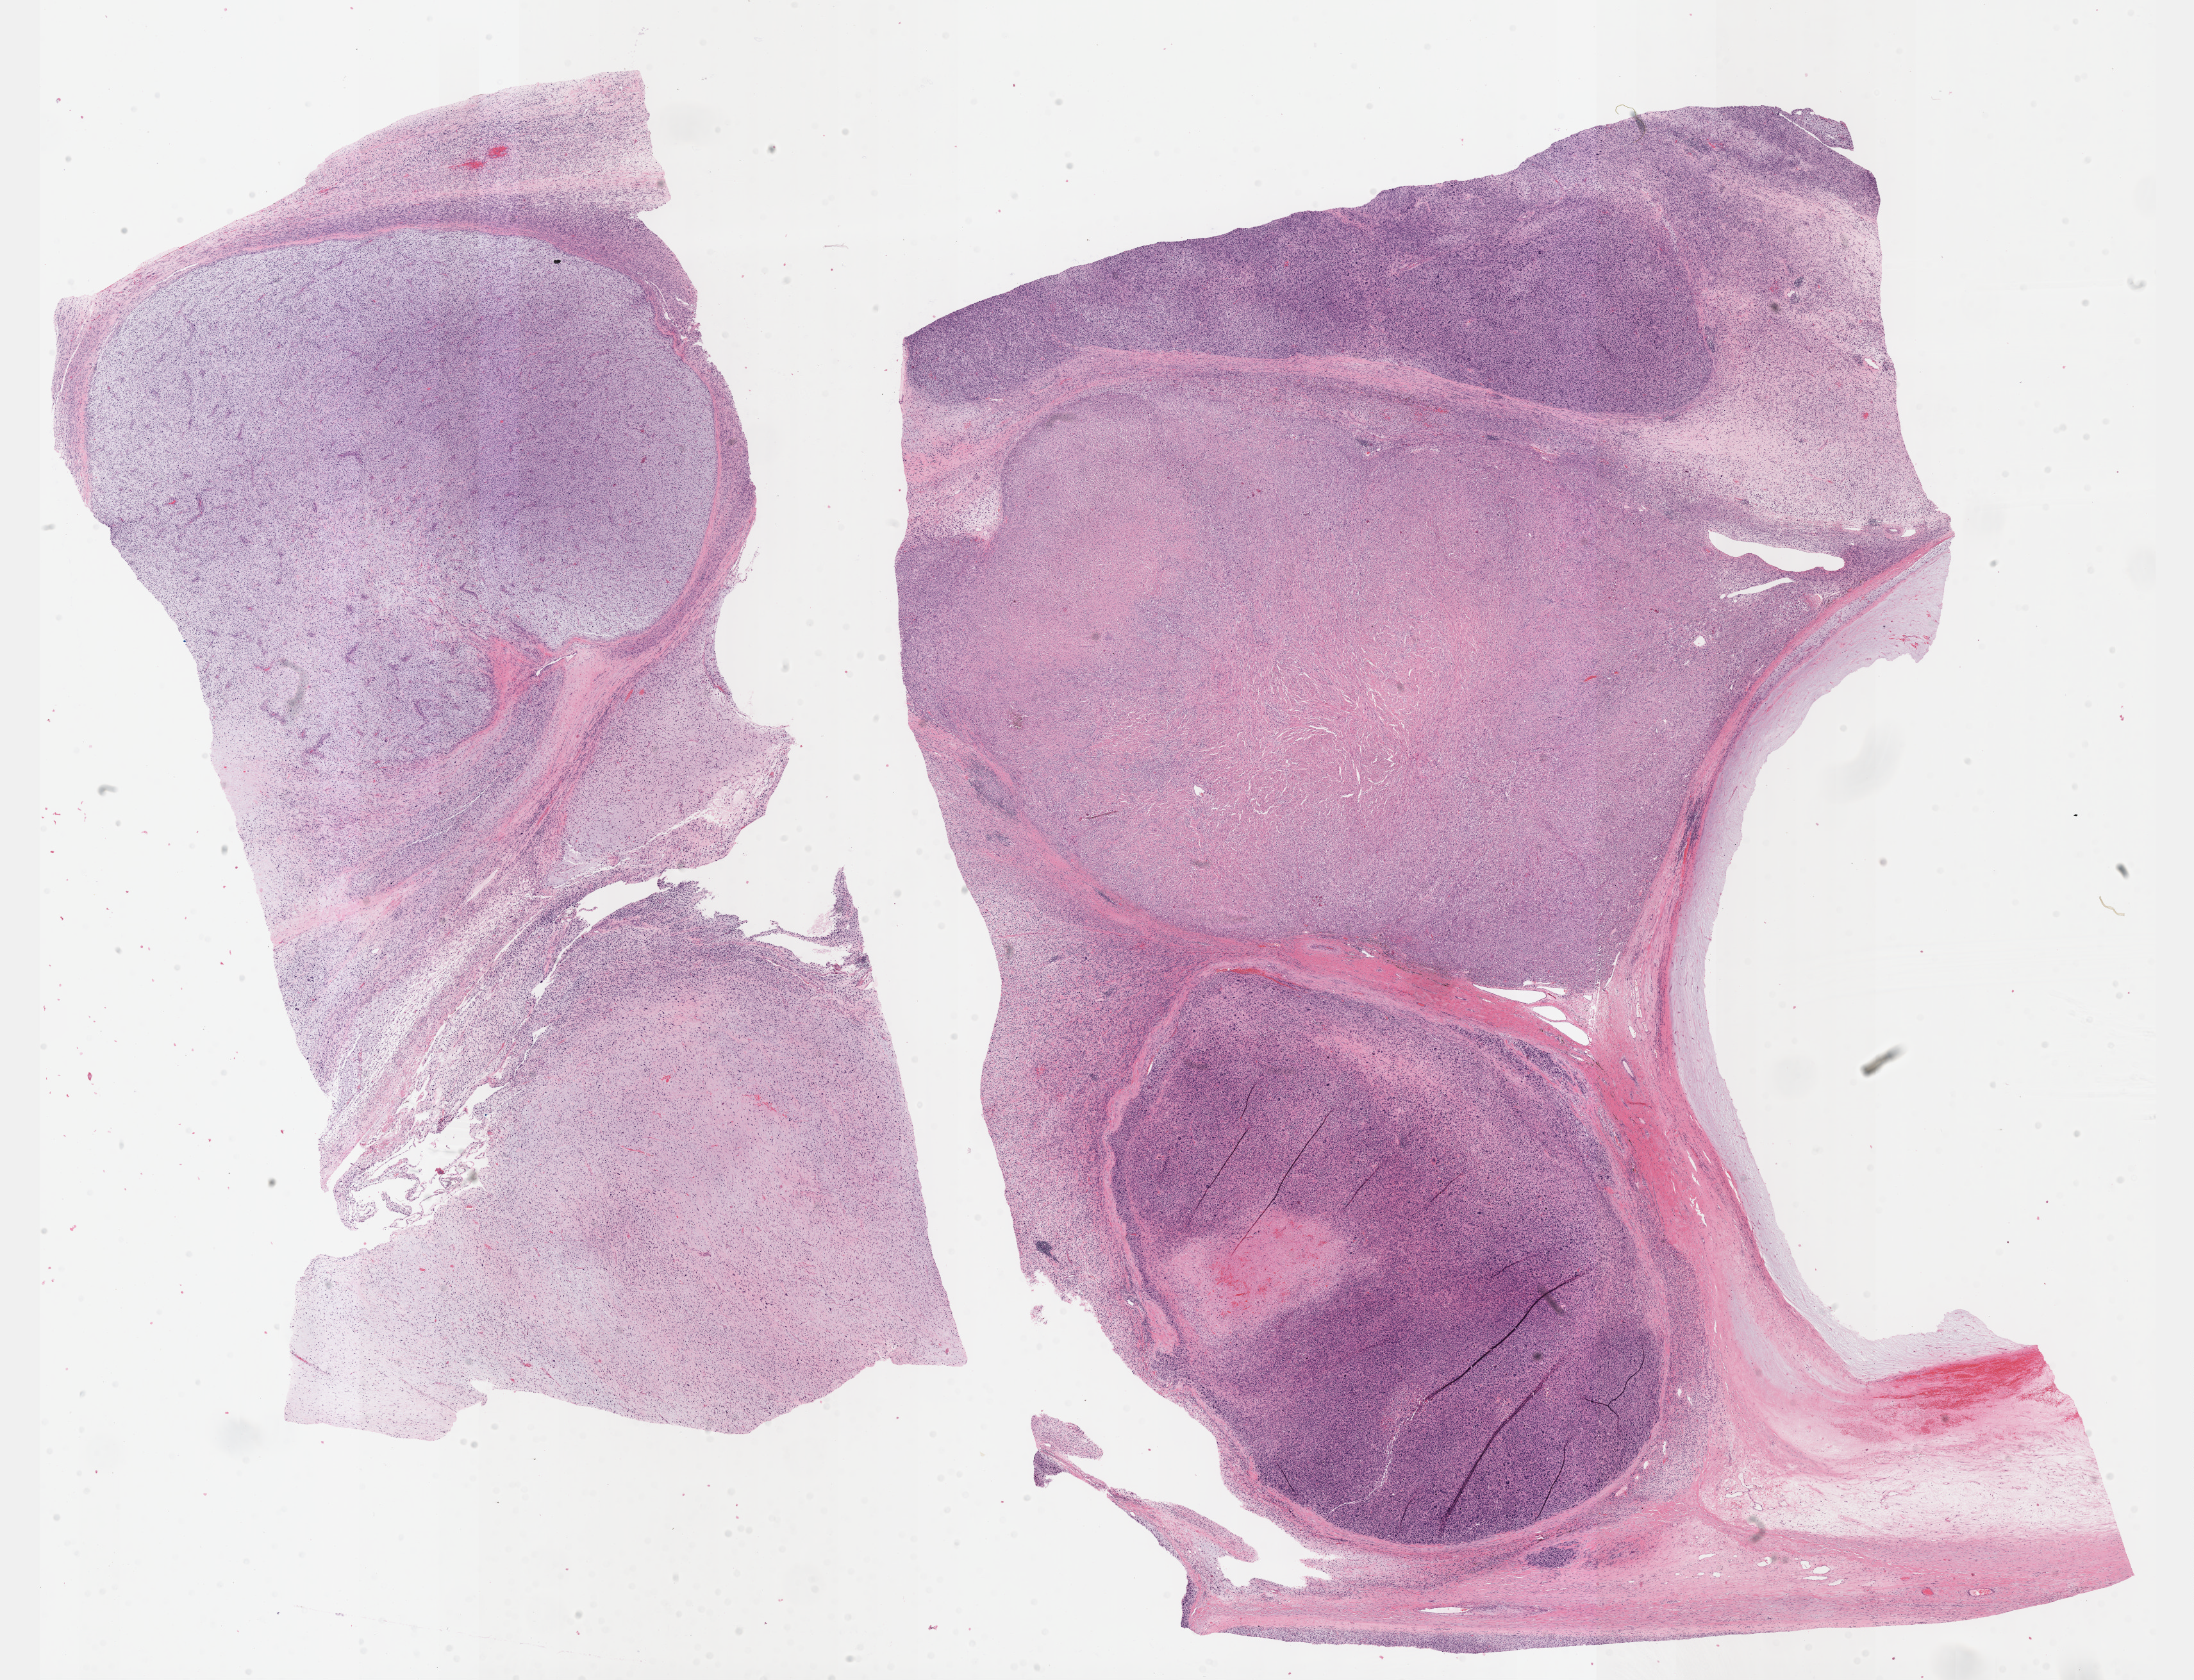
Digitized H&E tissue section (whole slide), a low-resolution overview of the entire scanned area, about 27.7 x 21.2 mm (acquisition: 40x scan), formalin-fixed paraffin-embedded (FFPE) diagnostic section, primary tumour sample from the connective, subcutaneous and other soft tissues. Male patient.
* diagnosis: Fibromyxosarcoma (connective, subcutaneous and other soft tissues of lower limb and hip)